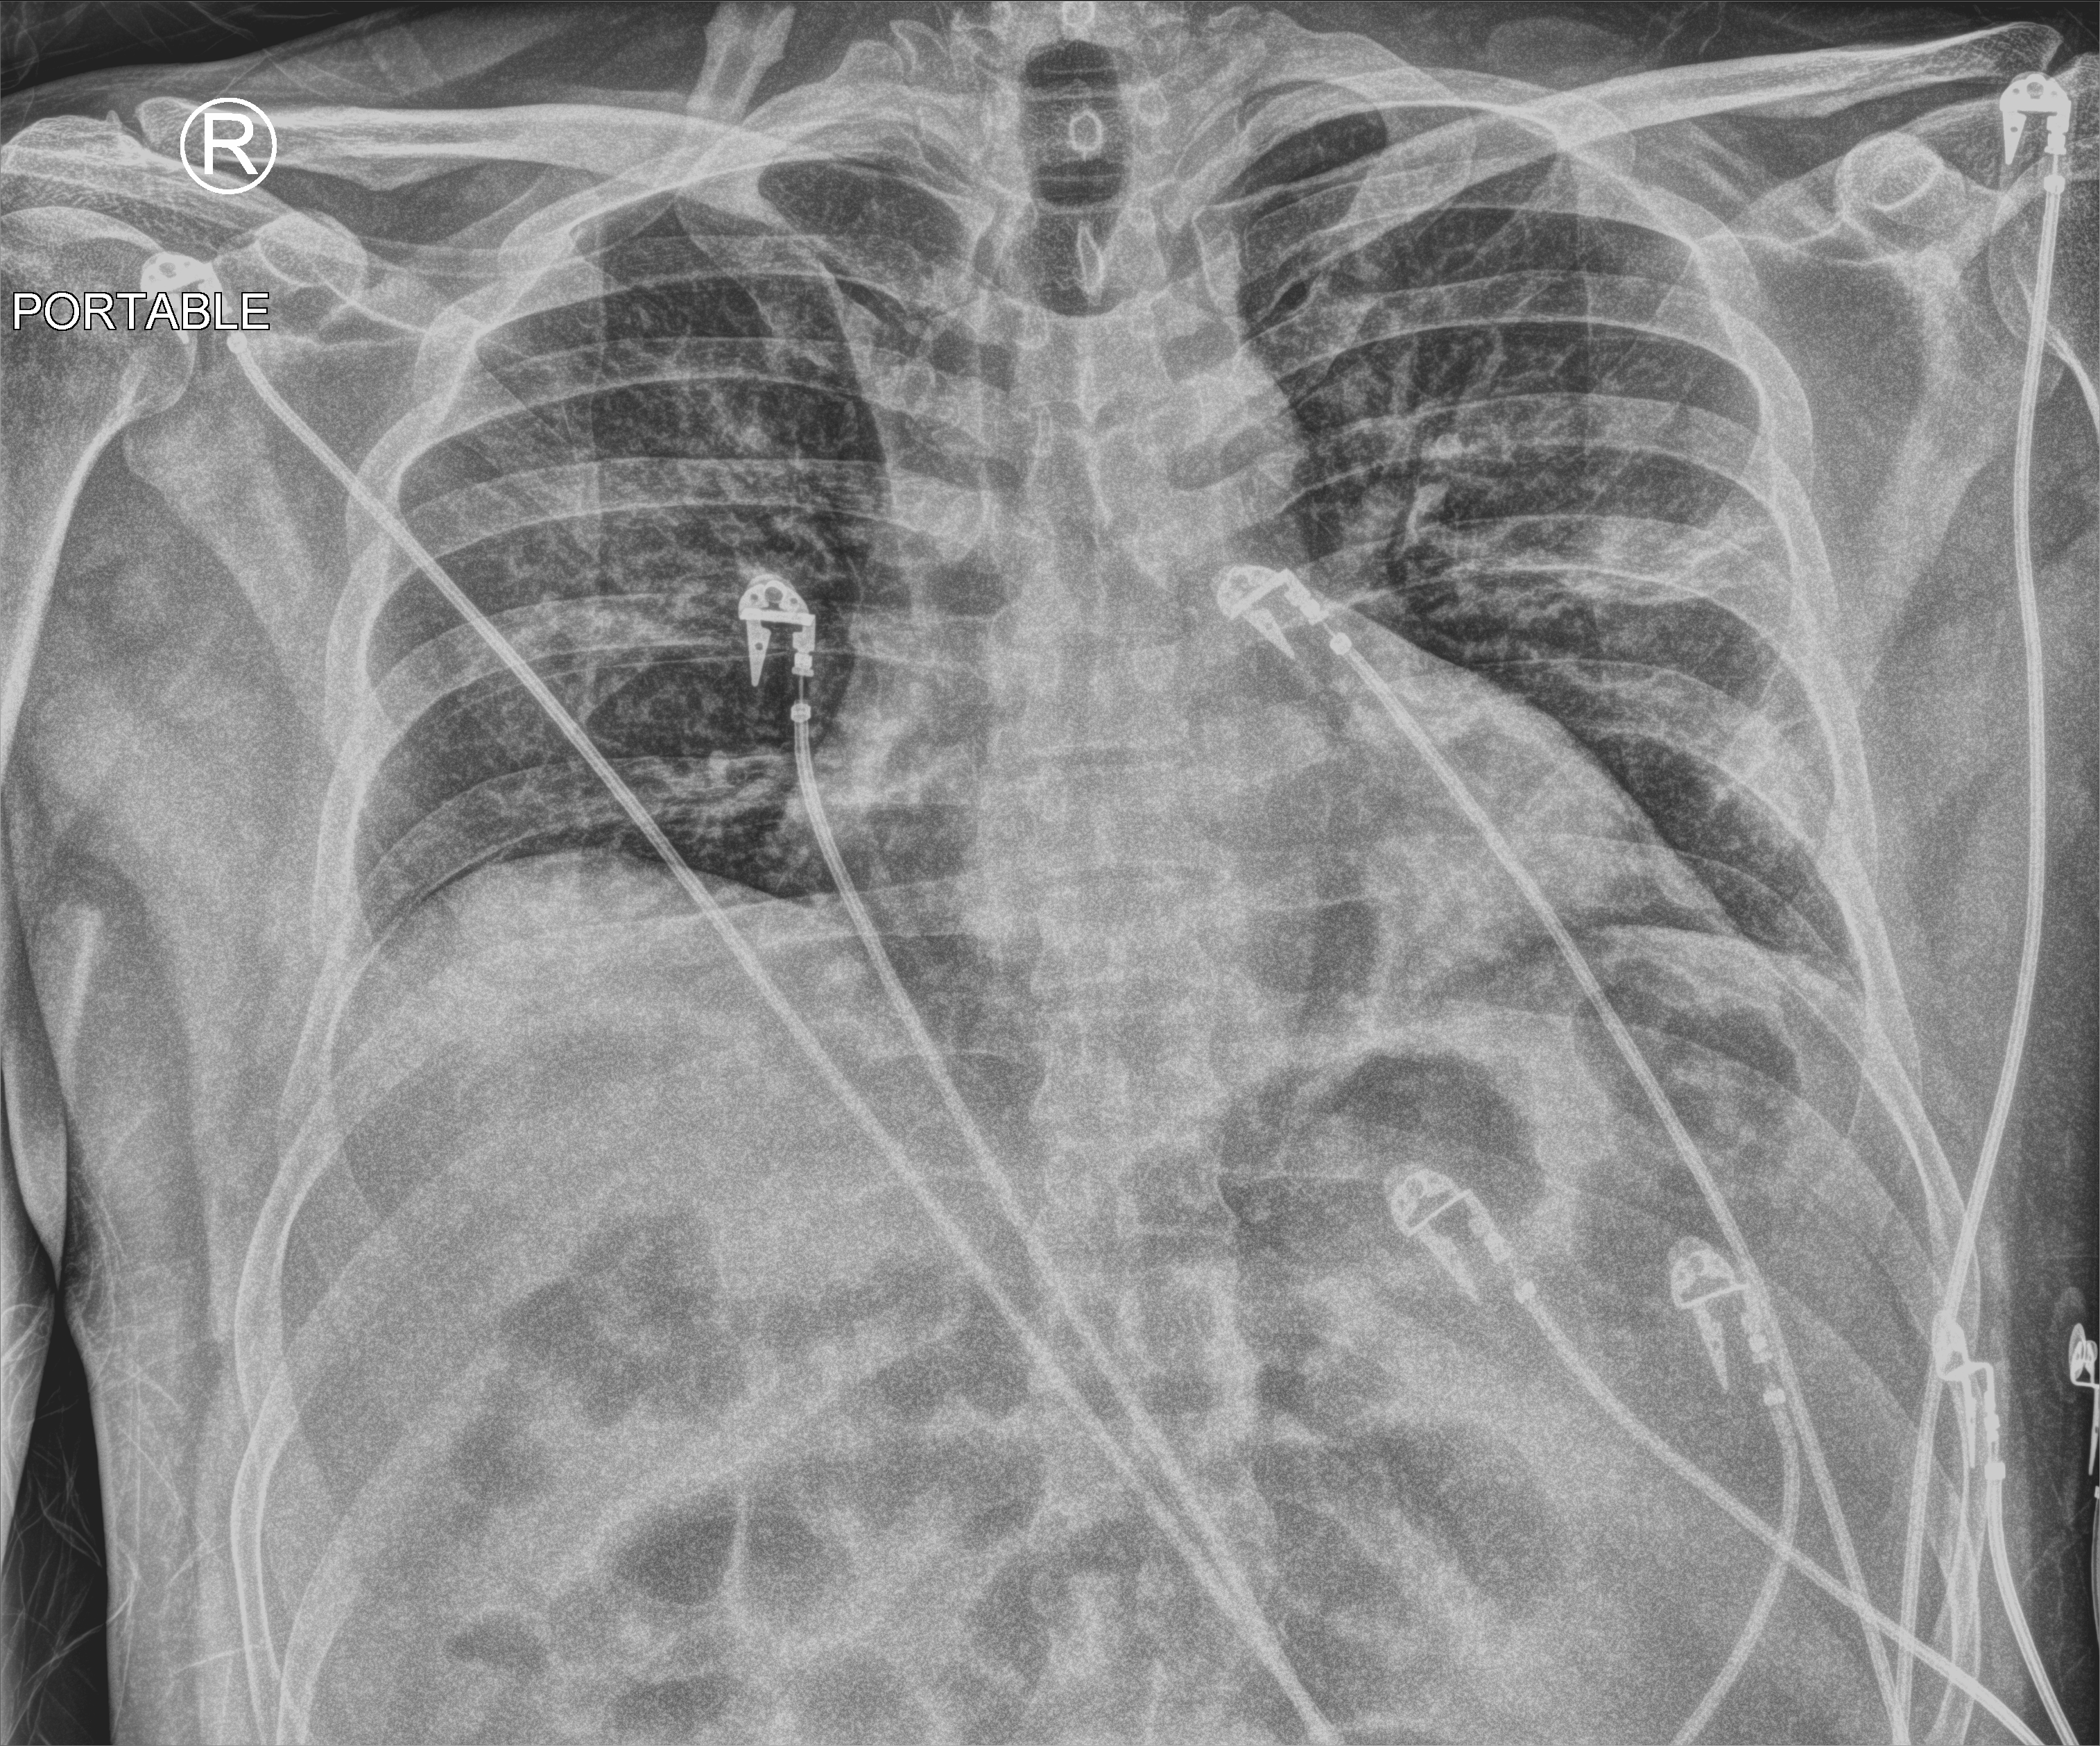
Bedside chest radiograph (computed radiography), anteroposterior (AP) projection. Patient hospitalised with COVID-19; male, aged 18–59 years.
Admission-level facts for this patient (not findings on this image; timing relative to this image not recorded): admitted to intensive care during this hospital stay: no; mechanically ventilated during this hospital stay: no.